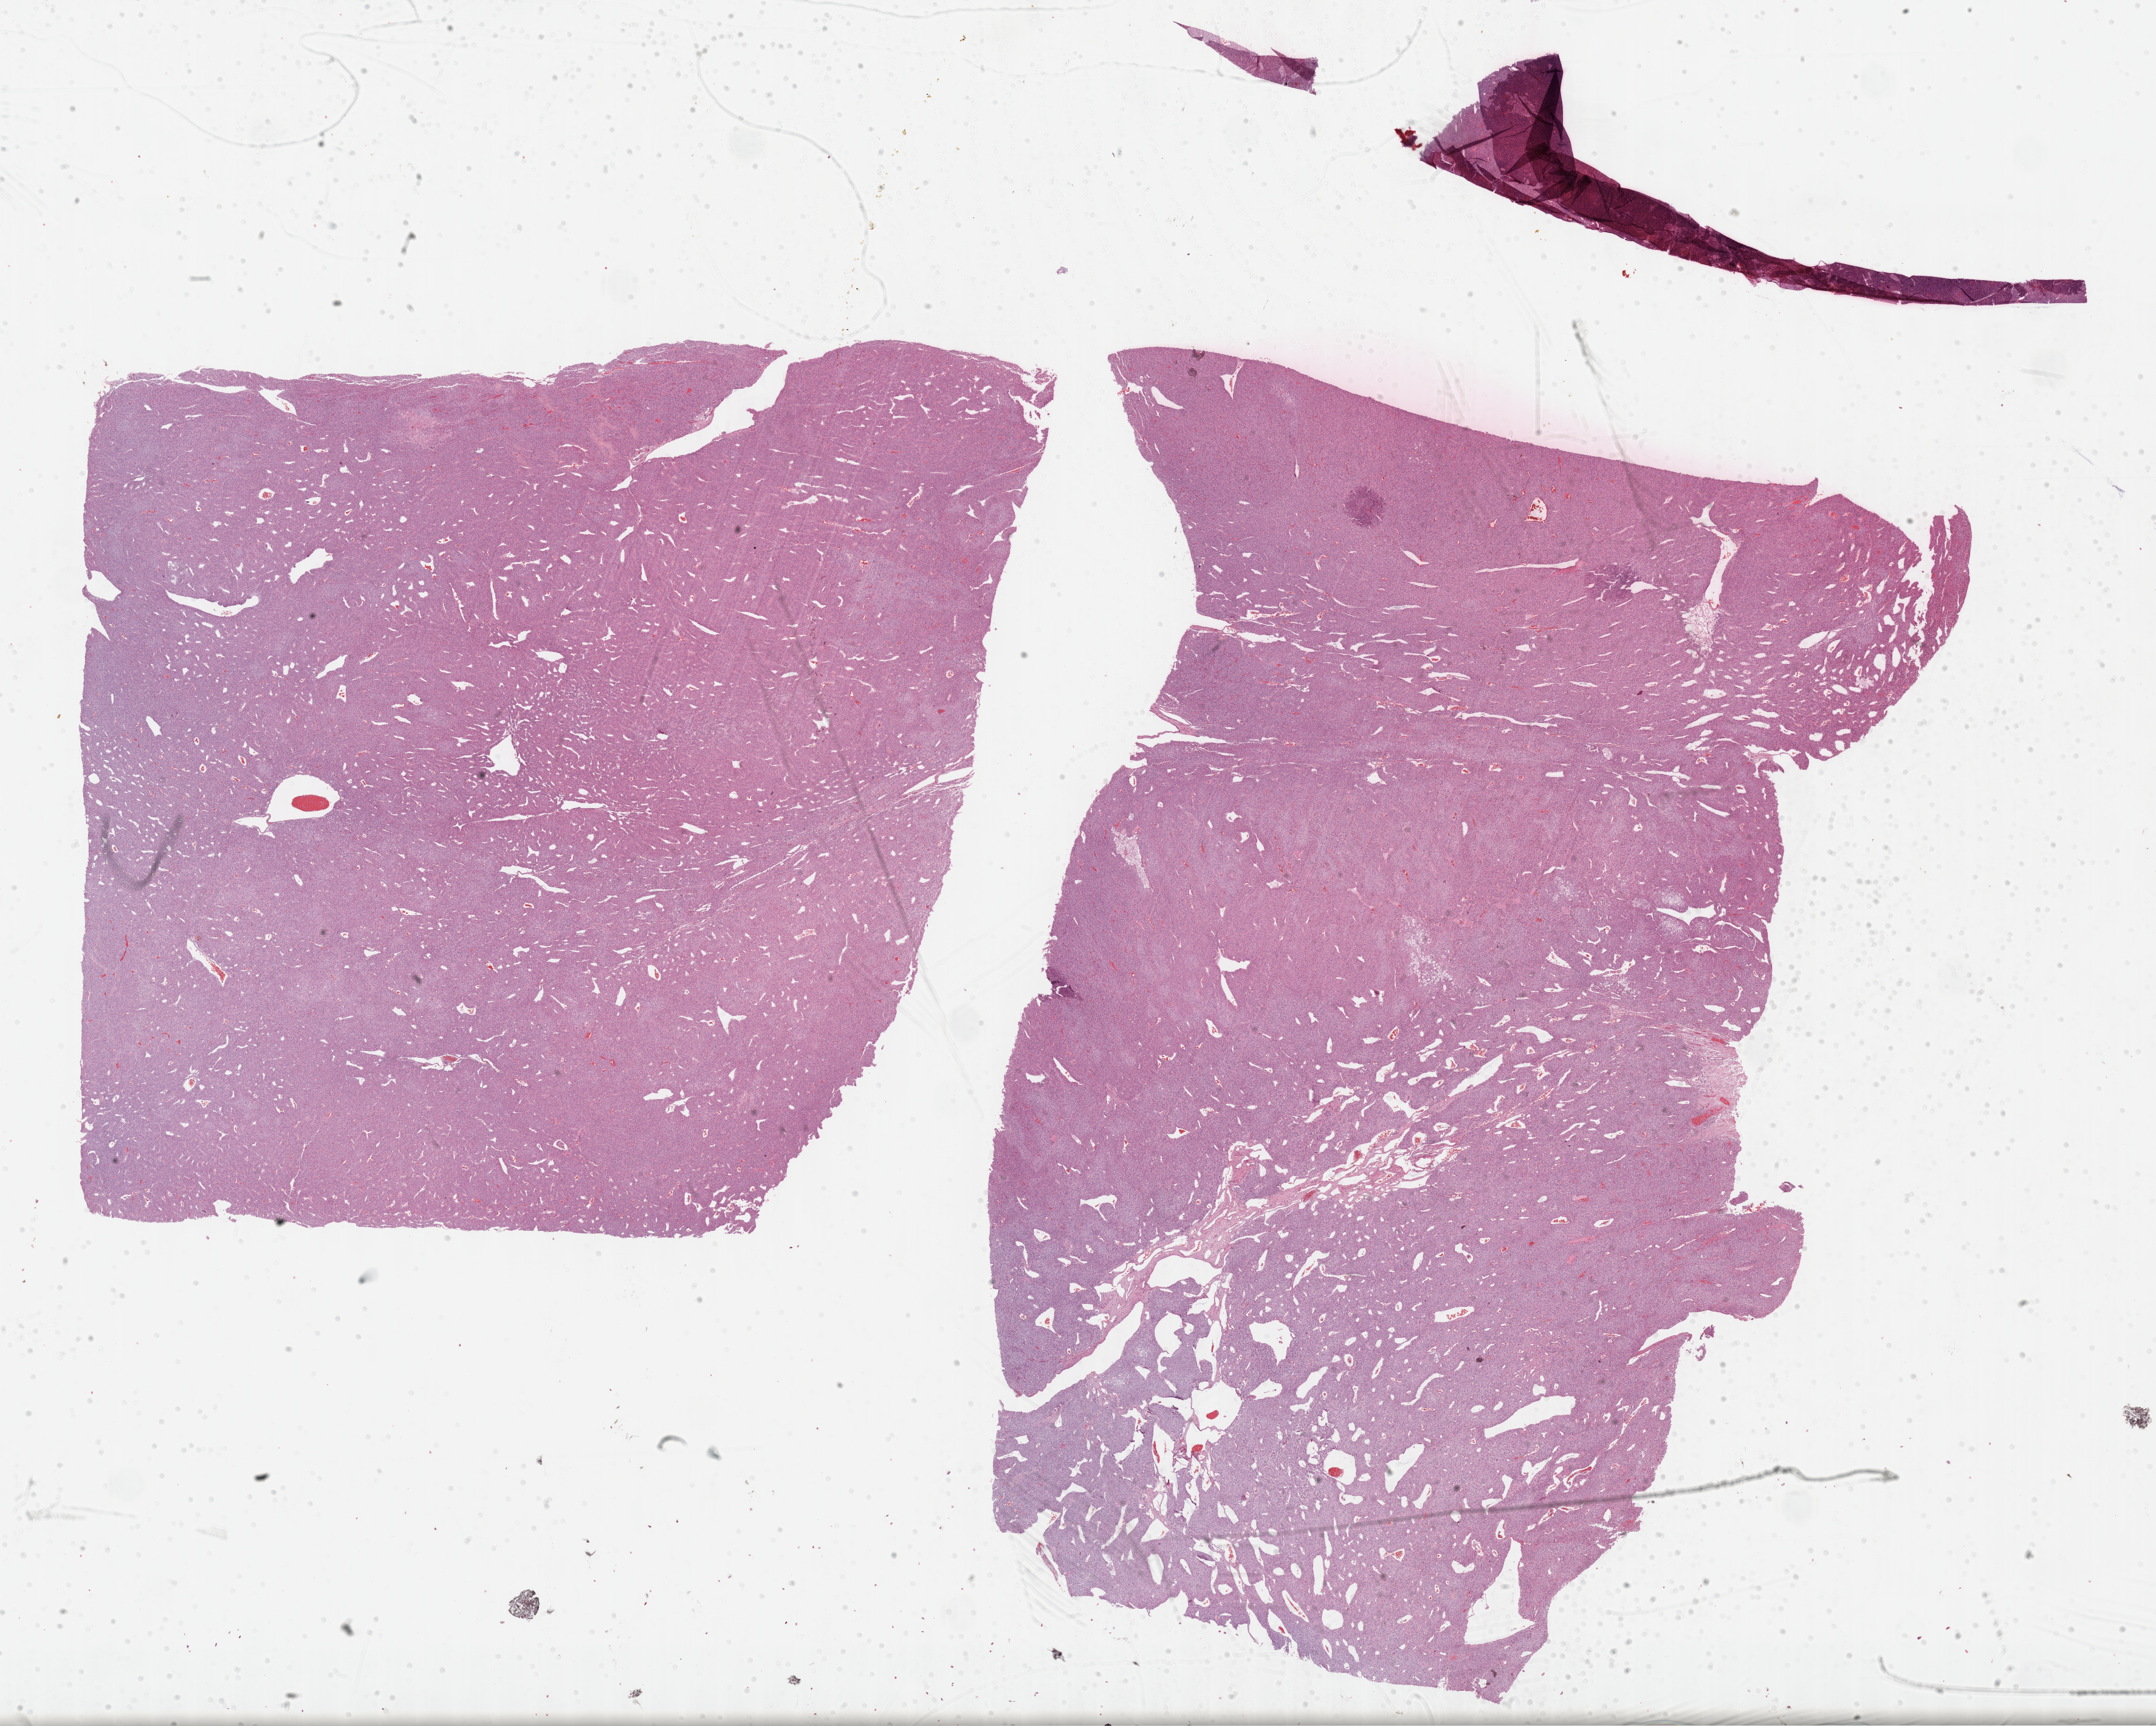
Digitized H&E tissue section (whole slide), a low-resolution overview of the entire scanned area, about 28.7 x 23.0 mm. Formalin-fixed paraffin-embedded (FFPE) diagnostic section. Primary tumour sample from the adrenal cortex. Patient: male, age at initial diagnosis 47 years.
Laterality: right. Histologic diagnosis: Adrenal cortical carcinoma.